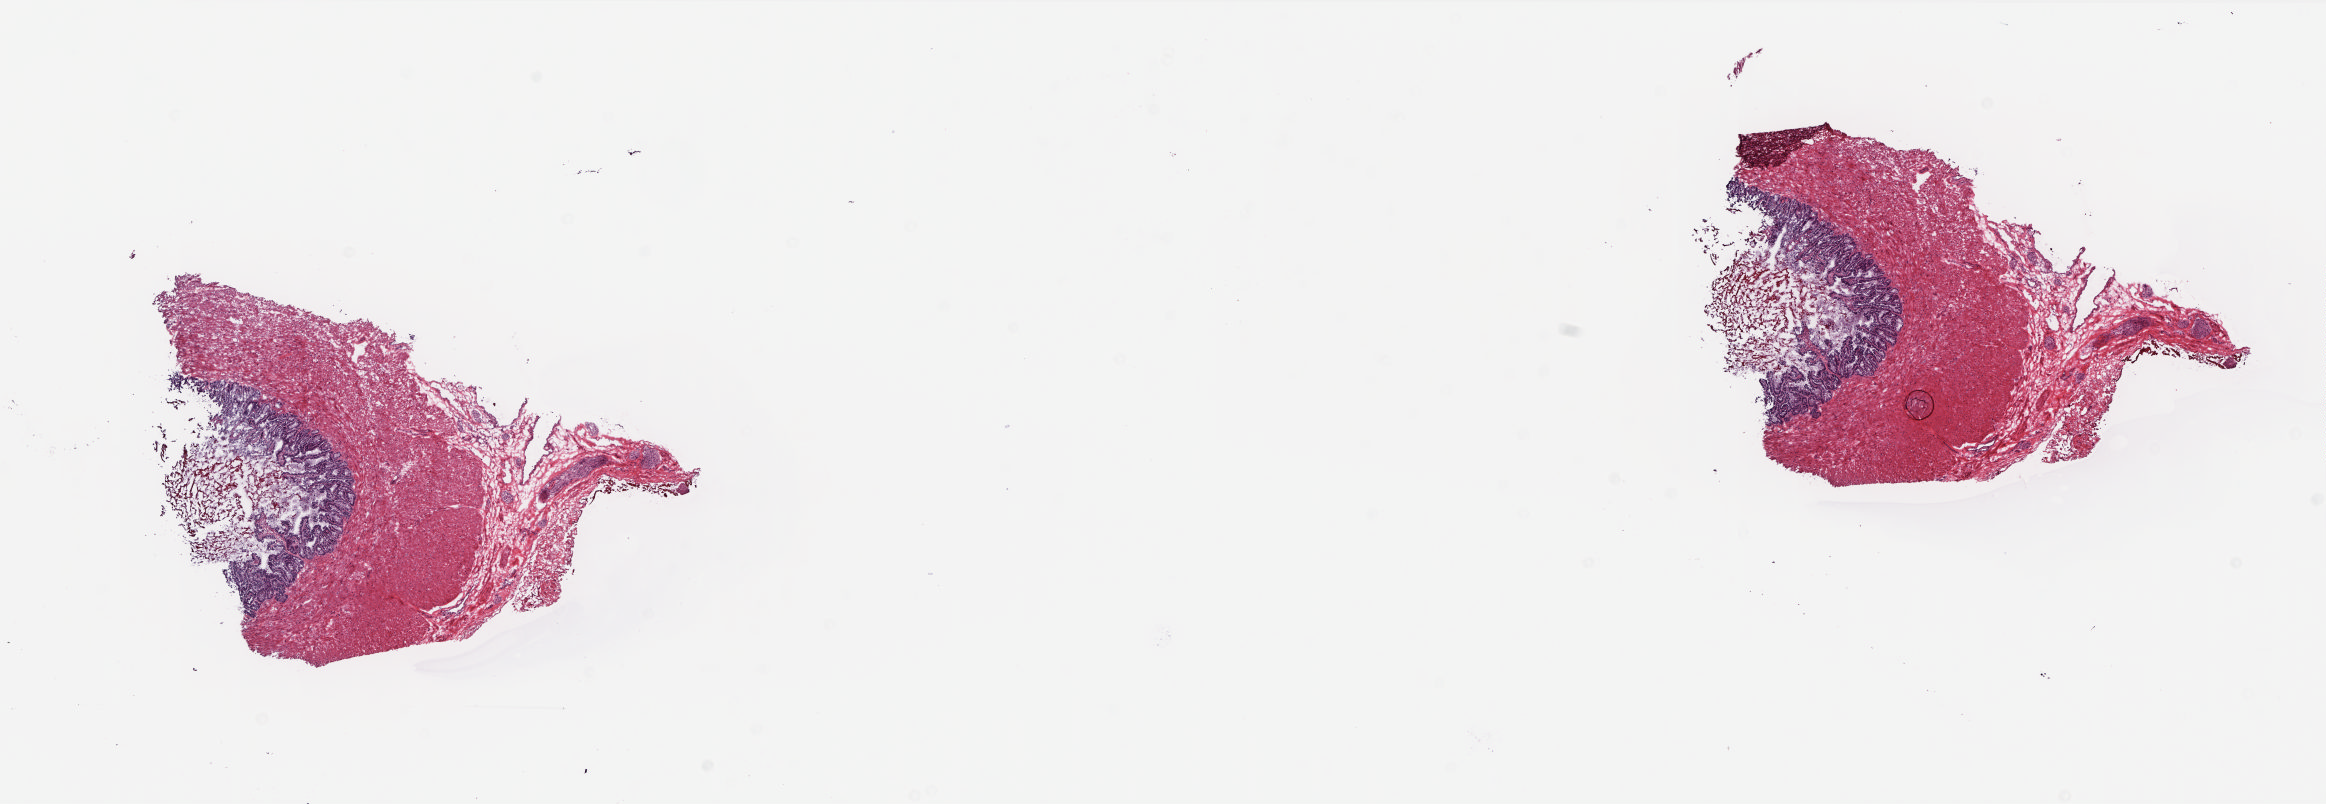
Digitized H&E-stained tissue section (whole slide) — shown as a low-resolution overview of the whole scanned area (about 18.8 x 6.5 mm, from a 20x scan). Frozen section from the top of the tissue portion. Sample: solid tissue normal (non-tumour tissue), prostate. Male patient; age at initial diagnosis 63 years. Slide review estimates, as recorded: tumour cells 0%, tumour nuclei 0%, normal cells 20%, stromal cells 80%, necrosis 0%. Inflammatory infiltration, as recorded: lymphocyte infiltration 2%, monocyte infiltration 0%, neutrophil infiltration 0%.
• this section: solid tissue normal sample (biorepository sample class)
• patient diagnosis: Adenocarcinoma, NOS (prostate gland)